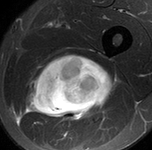
MRI of an extremity soft-tissue mass, one axial slice; position 74 of 90 along the scan axis; STIR; MR volume resampled by the dataset authors to the PET/CT grid (not the native acquisition matrix); 3.27 mm slice thickness; 152 × 150 image matrix. Male patient. Case-level facts recorded for this patient, not image findings: histological type: undifferentiated pleomorphic liposarcoma; grade: high; site of the primary tumour: left thigh.
Structures marked on this image (expert contour drawn on MRI and transferred to this co-registered scan by the dataset authors):
- gross tumour volume including surrounding oedema: bounding box (x1, y1, x2, y2) in pixels: (25, 53, 119, 124)
- gross tumour volume (mass): (34, 55, 117, 115)